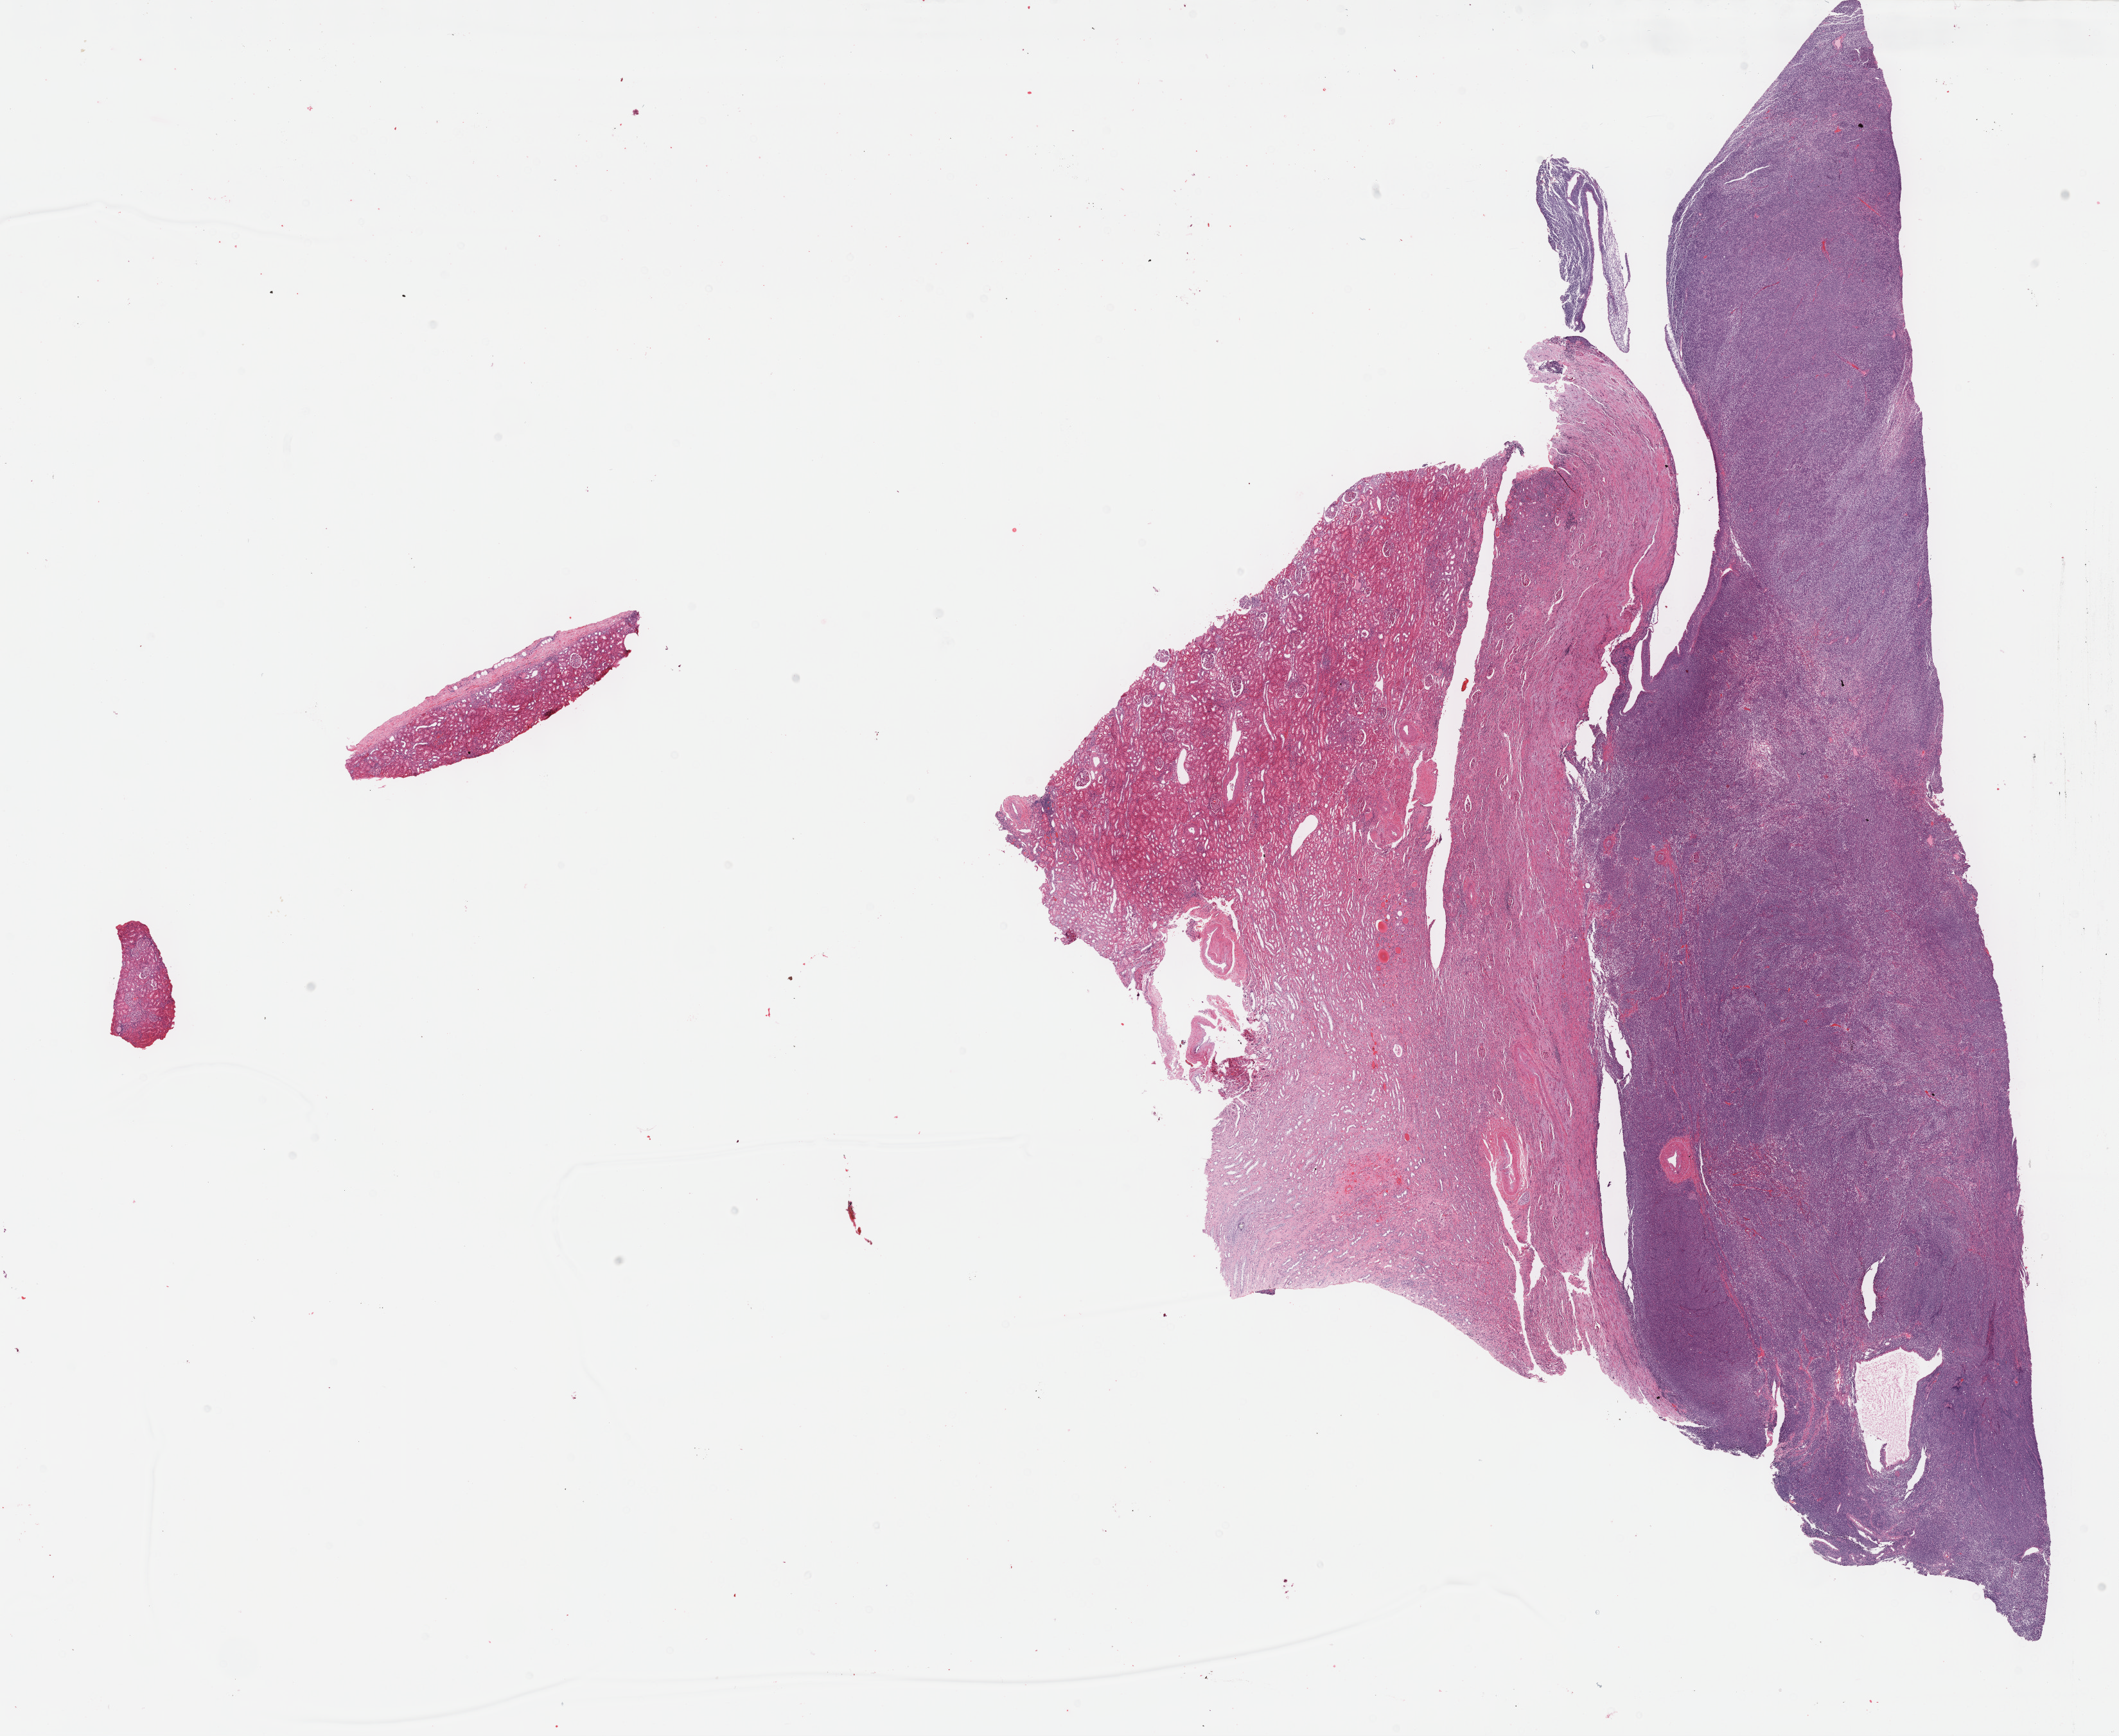
Hematoxylin and eosin (H&E) stained whole-slide image, a low-resolution overview of the entire scanned area, about 26.7 x 21.9 mm. Formalin-fixed paraffin-embedded (FFPE) diagnostic section. Primary tumour sample from the kidney. Patient: female, age at initial diagnosis 40 years.
Diagnosis: Synovial sarcoma, spindle cell.